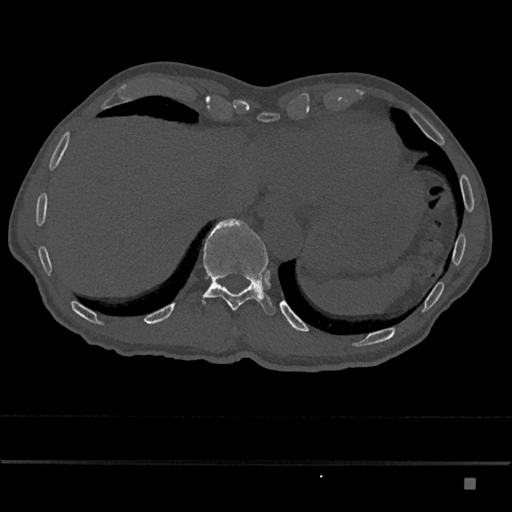
CT including the spine, one axial slice; position 681 of 797 along the scan axis; reconstruction kernel Br40s/3; 120 kVp; bone window (W 1800 / L 400 HU); 512 × 512 image matrix. Male patient, age 72 years. From the clinical record (not read from this slice): primary cancer: prostate.
Annotated regions visible in this slice (semi-automatic segmentation, software-assisted and operator-edited):
- T11 vertebra: bounding box [x1, y1, x2, y2] px = [203, 218, 275, 315]